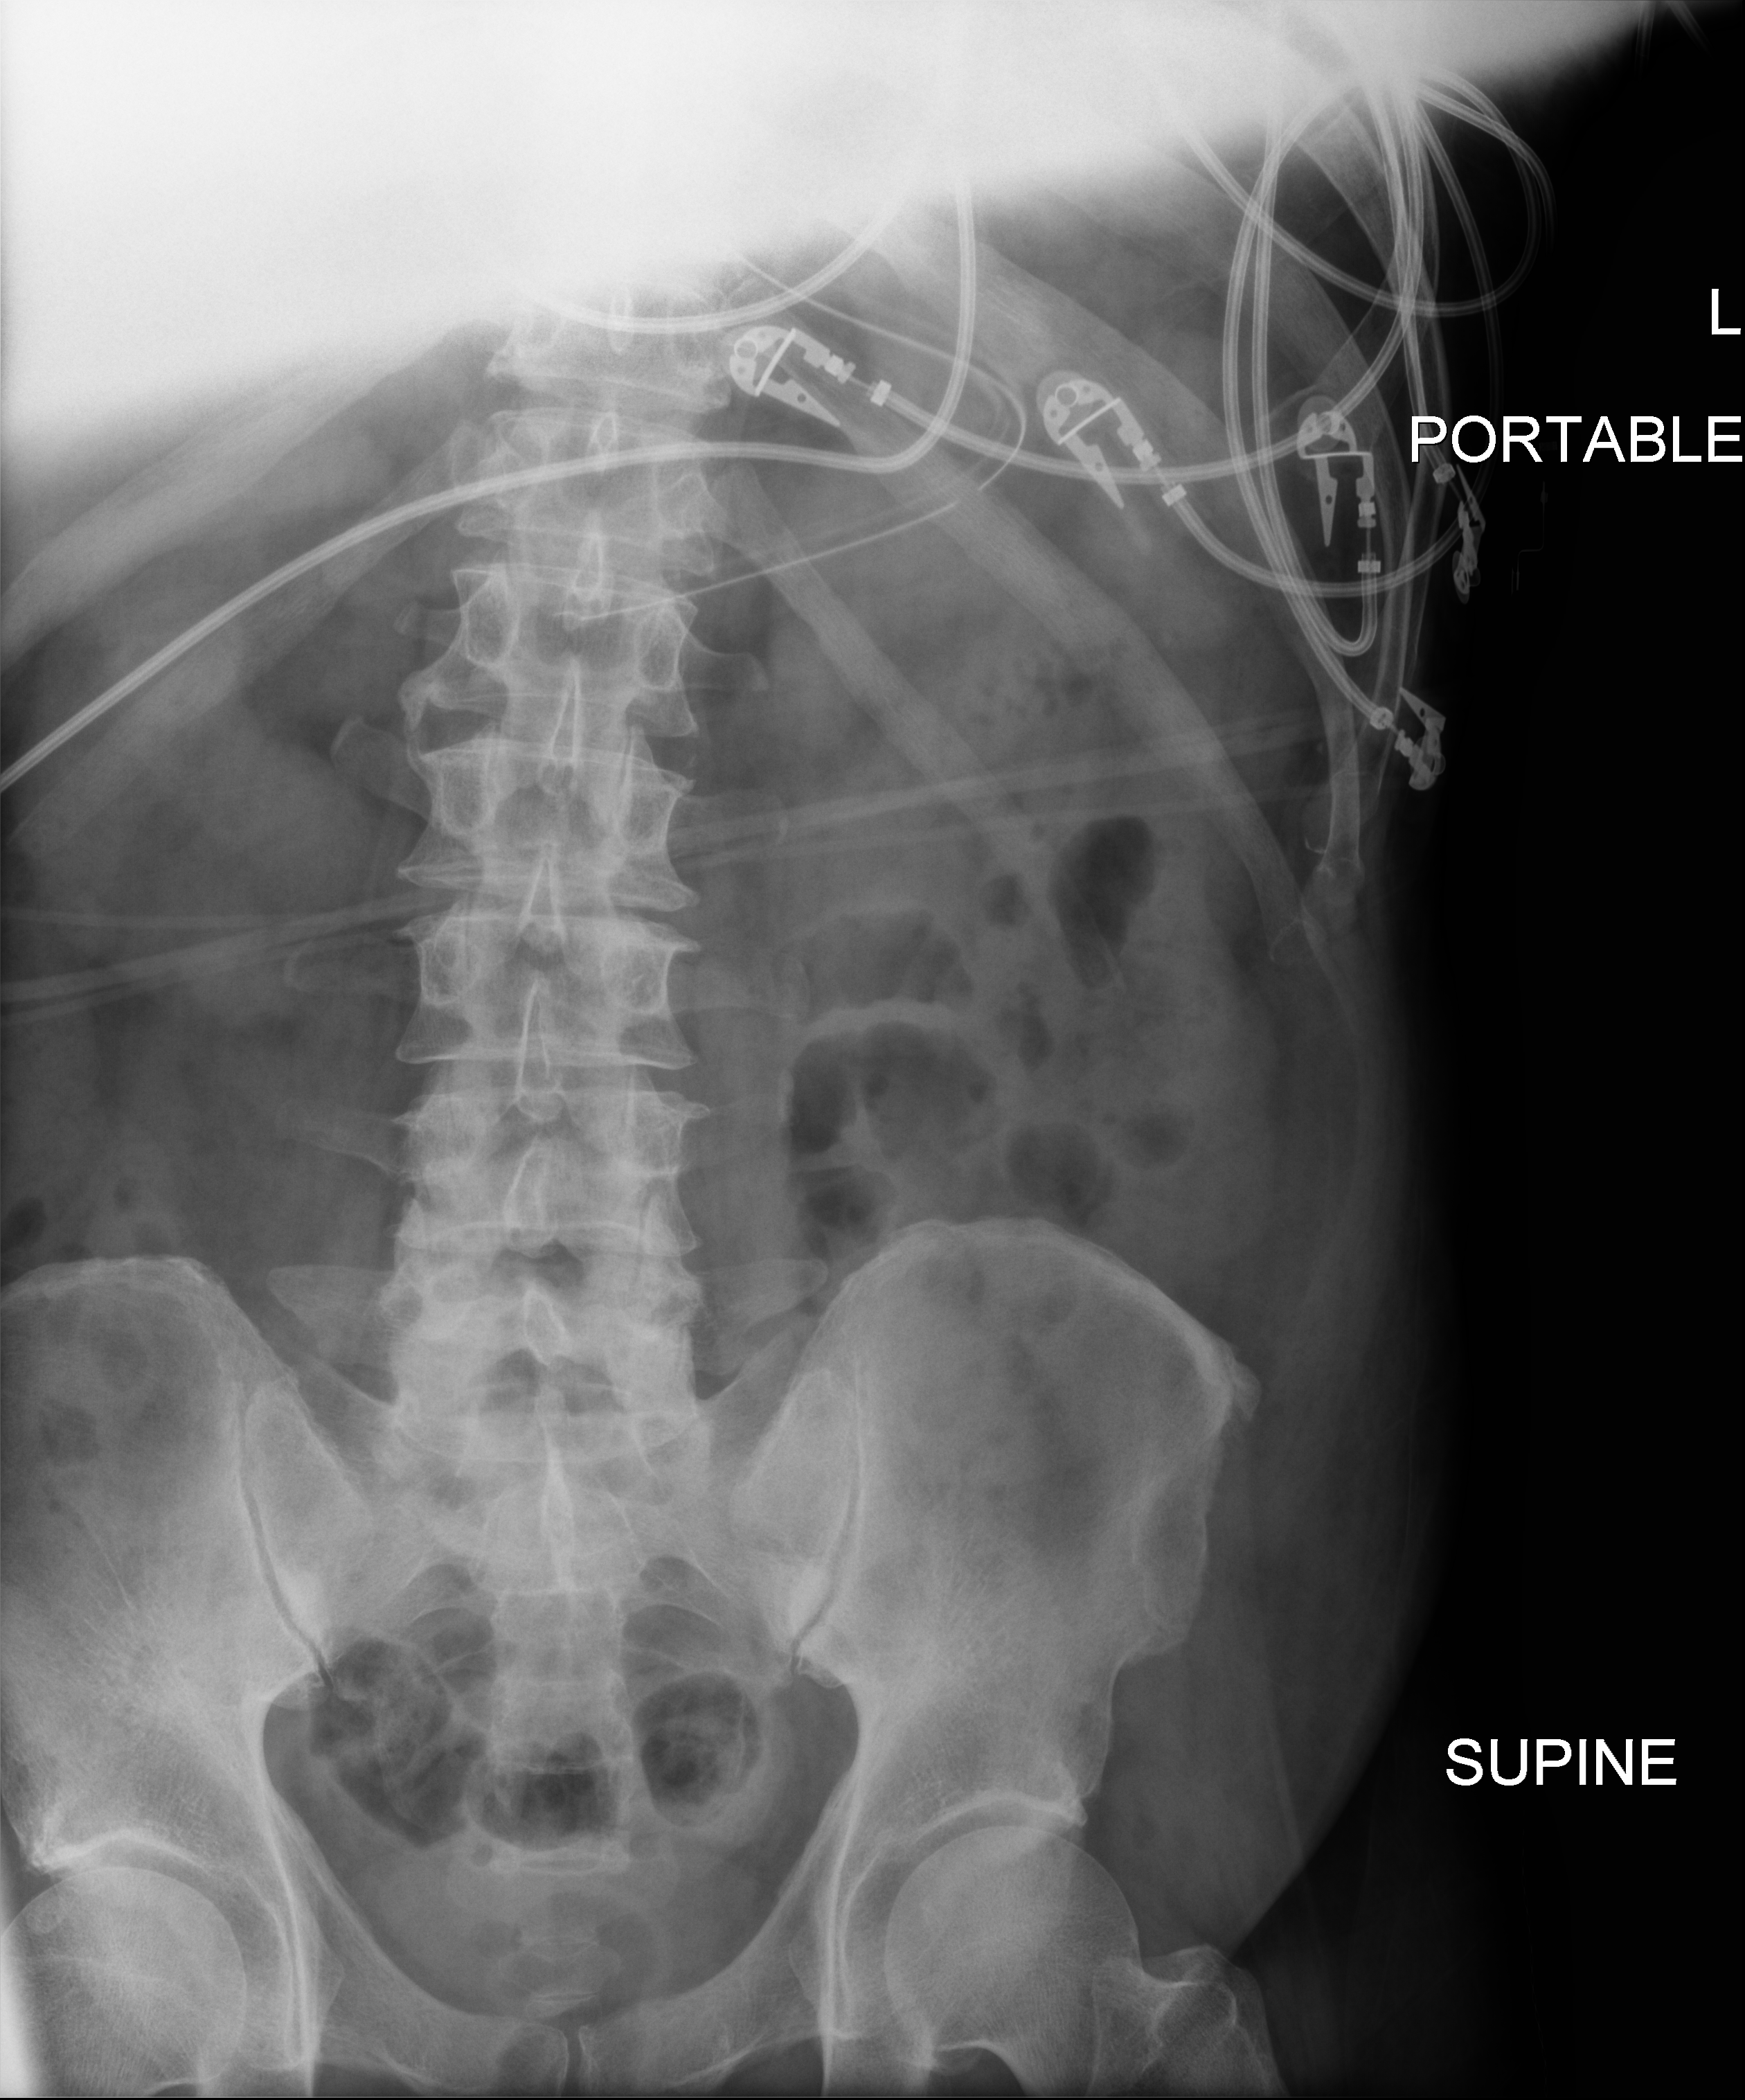
Bedside abdomen radiograph (digital radiography); anteroposterior (AP) projection. Male patient hospitalised with COVID-19, age 18–59 years.
From the hospital-stay record, not from the radiograph (when in the stay this image was taken is not recorded): smoking status (admission record): never; admitted to intensive care during this hospital stay: yes; COPD (admission record): no.